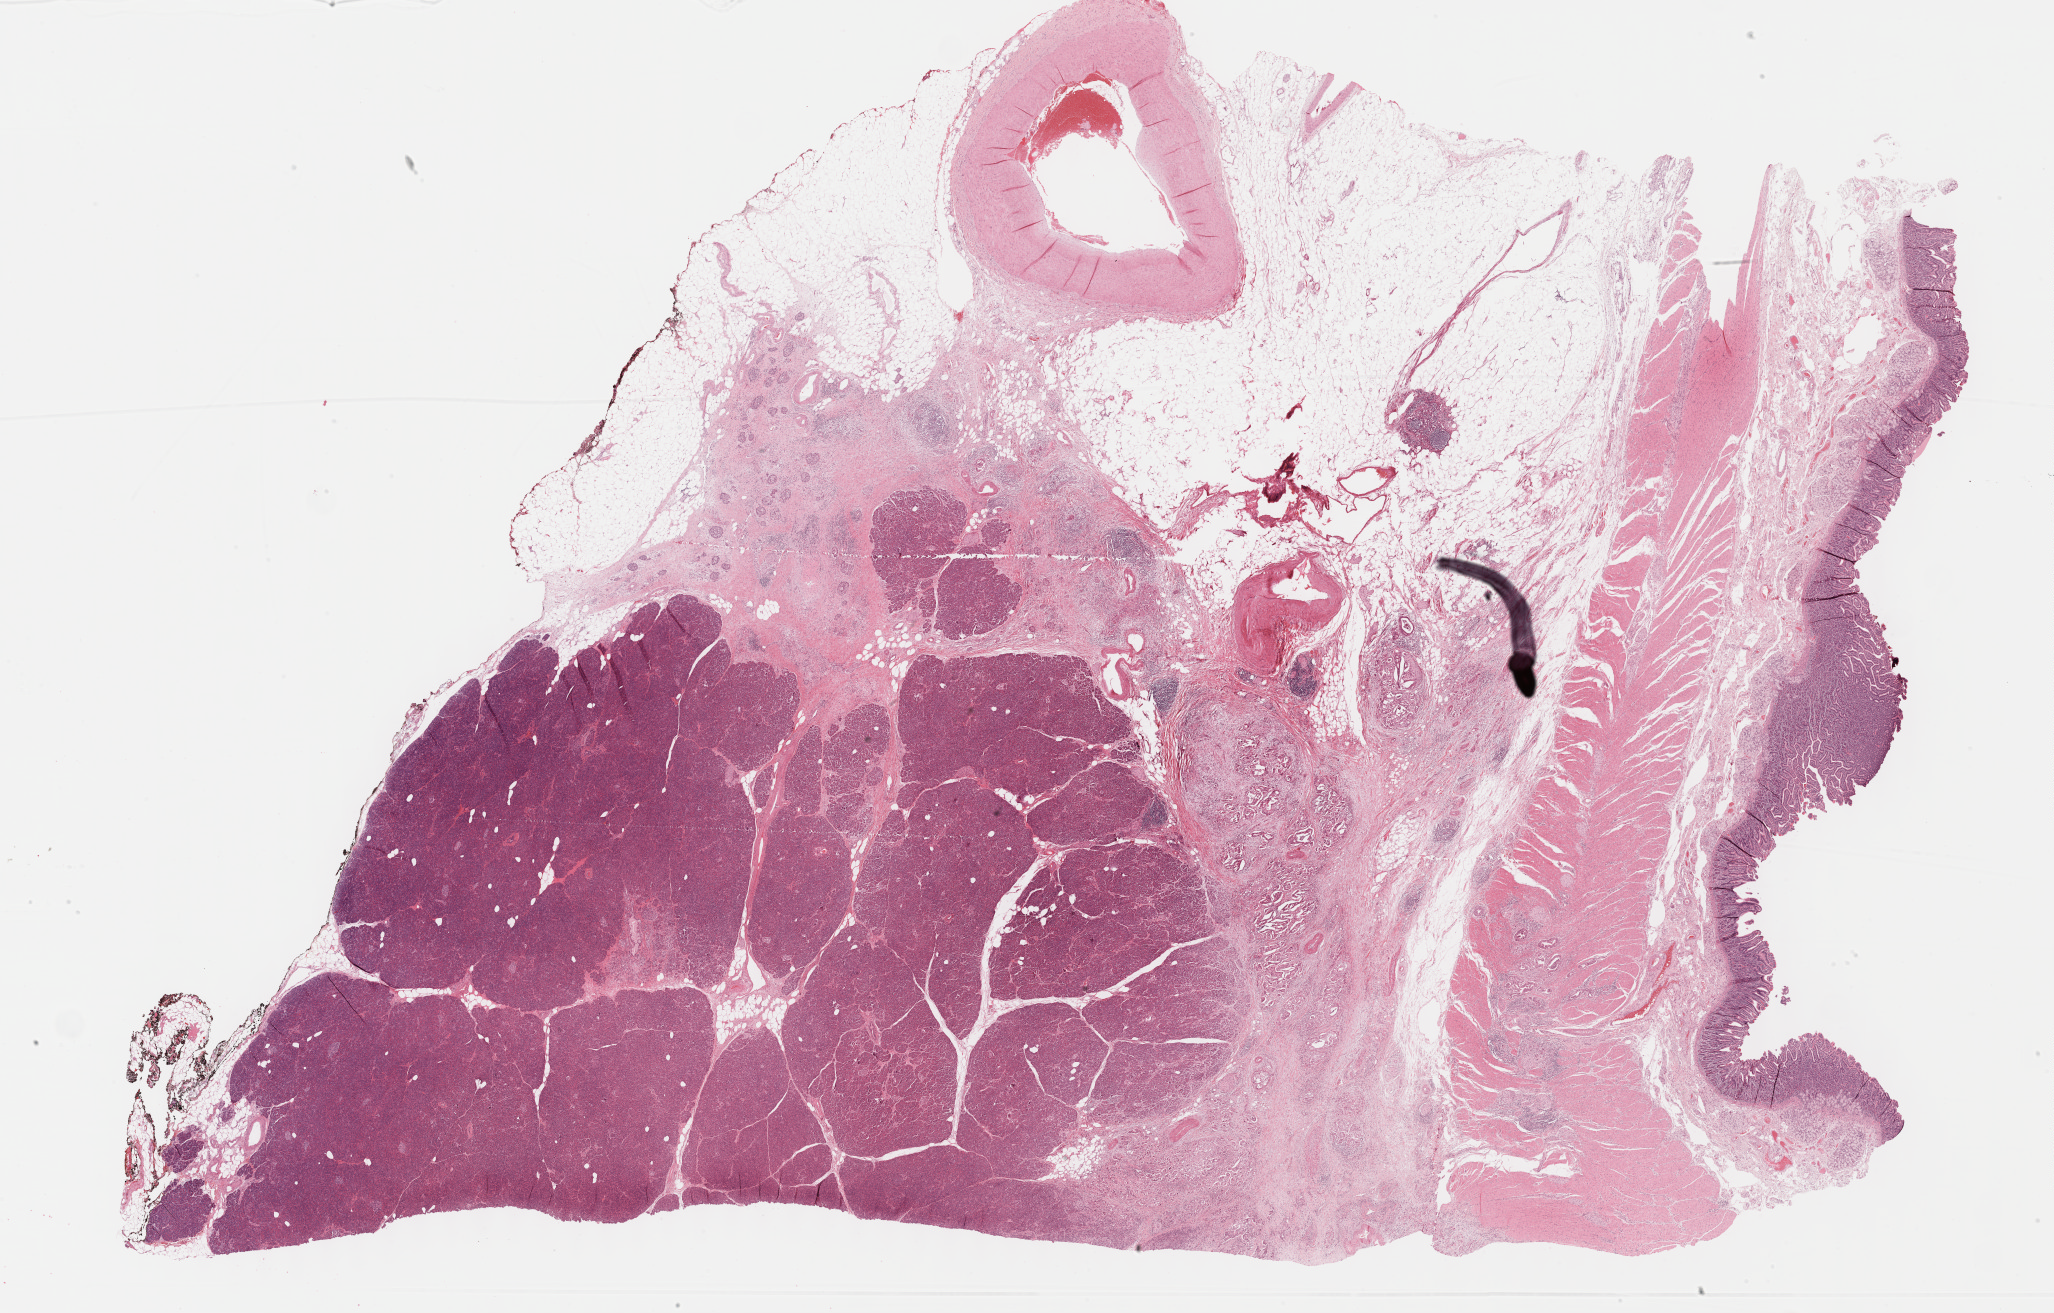
Hematoxylin and eosin (H&E) stained whole-slide image, shown as a low-resolution overview of the whole scanned area (about 33.2 x 21.2 mm, acquisition: 40x scan), FFPE section, primary tumour sample from the pancreas. Female, age 64 years at initial diagnosis.
Pathologic diagnosis: Infiltrating duct carcinoma, NOS (head of pancreas).